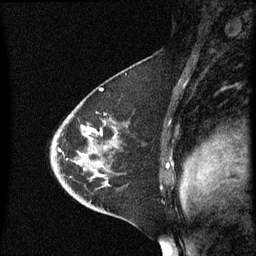
Breast MRI (dynamic contrast-enhanced), one sagittal slice. Position 39 of 60 along the scan axis. Dynamic contrast-enhanced series, image 2 of 3 at this slice position (ordered by acquisition). 1.5 T. TE 4.2 ms, TR 8.4 ms. 2.3 mm slice thickness. 256 × 256 image matrix, field of view 200 × 200 mm. Patient: female, 46 years. From the clinical record (not read from this slice): setting: breast cancer imaged before/during neoadjuvant chemotherapy; receptor status: HER2-positive.
Annotated regions visible in this slice (semi-automatic segmentation, software-assisted and operator-edited):
- analysis volume of interest (the breast-tissue region the enhancement analysis was run in; not a lesion): box from (x=51, y=96) to (x=167, y=187) px
- tumour enhancement mask (voxels above the 70 % enhancement threshold inside the analysis volume of interest): (x=59, y=126)–(x=95, y=161)